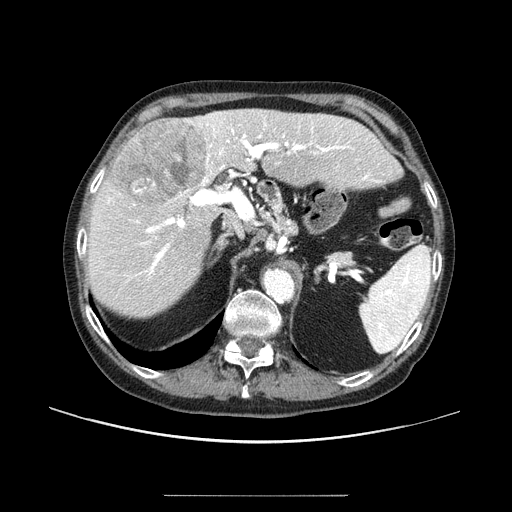
Contrast-enhanced abdominal CT (liver protocol), one axial slice. Position 58 of 91 along the scan axis. Reconstruction kernel STANDARD. 100 kVp. One of 2 acquisitions stored at this slice position. Soft-tissue window (W 400 / L 40 HU). 2.5 mm slice thickness. 512 × 512 image matrix, field of view 400 × 400 mm. Case-level facts recorded for this patient, not image findings: diagnosis: hepatocellular carcinoma (patient treated with transarterial chemoembolisation; whether this scan precedes or follows treatment is not stated here); TNM stage (as recorded): Stage-I; Child-Pugh class: A; tumour differentiation: moderately differentiated.
Structures marked on this image (semi-automatically segmented with operator editing):
- liver parenchyma outside the tumour (the mass and vessels are separate outlines, so this box may not span the whole liver): bounding box <86,108,400,316> (left, top, right, bottom; pixels)
- mass: <110,118,209,209>
- liver vessels: <94,112,381,281>